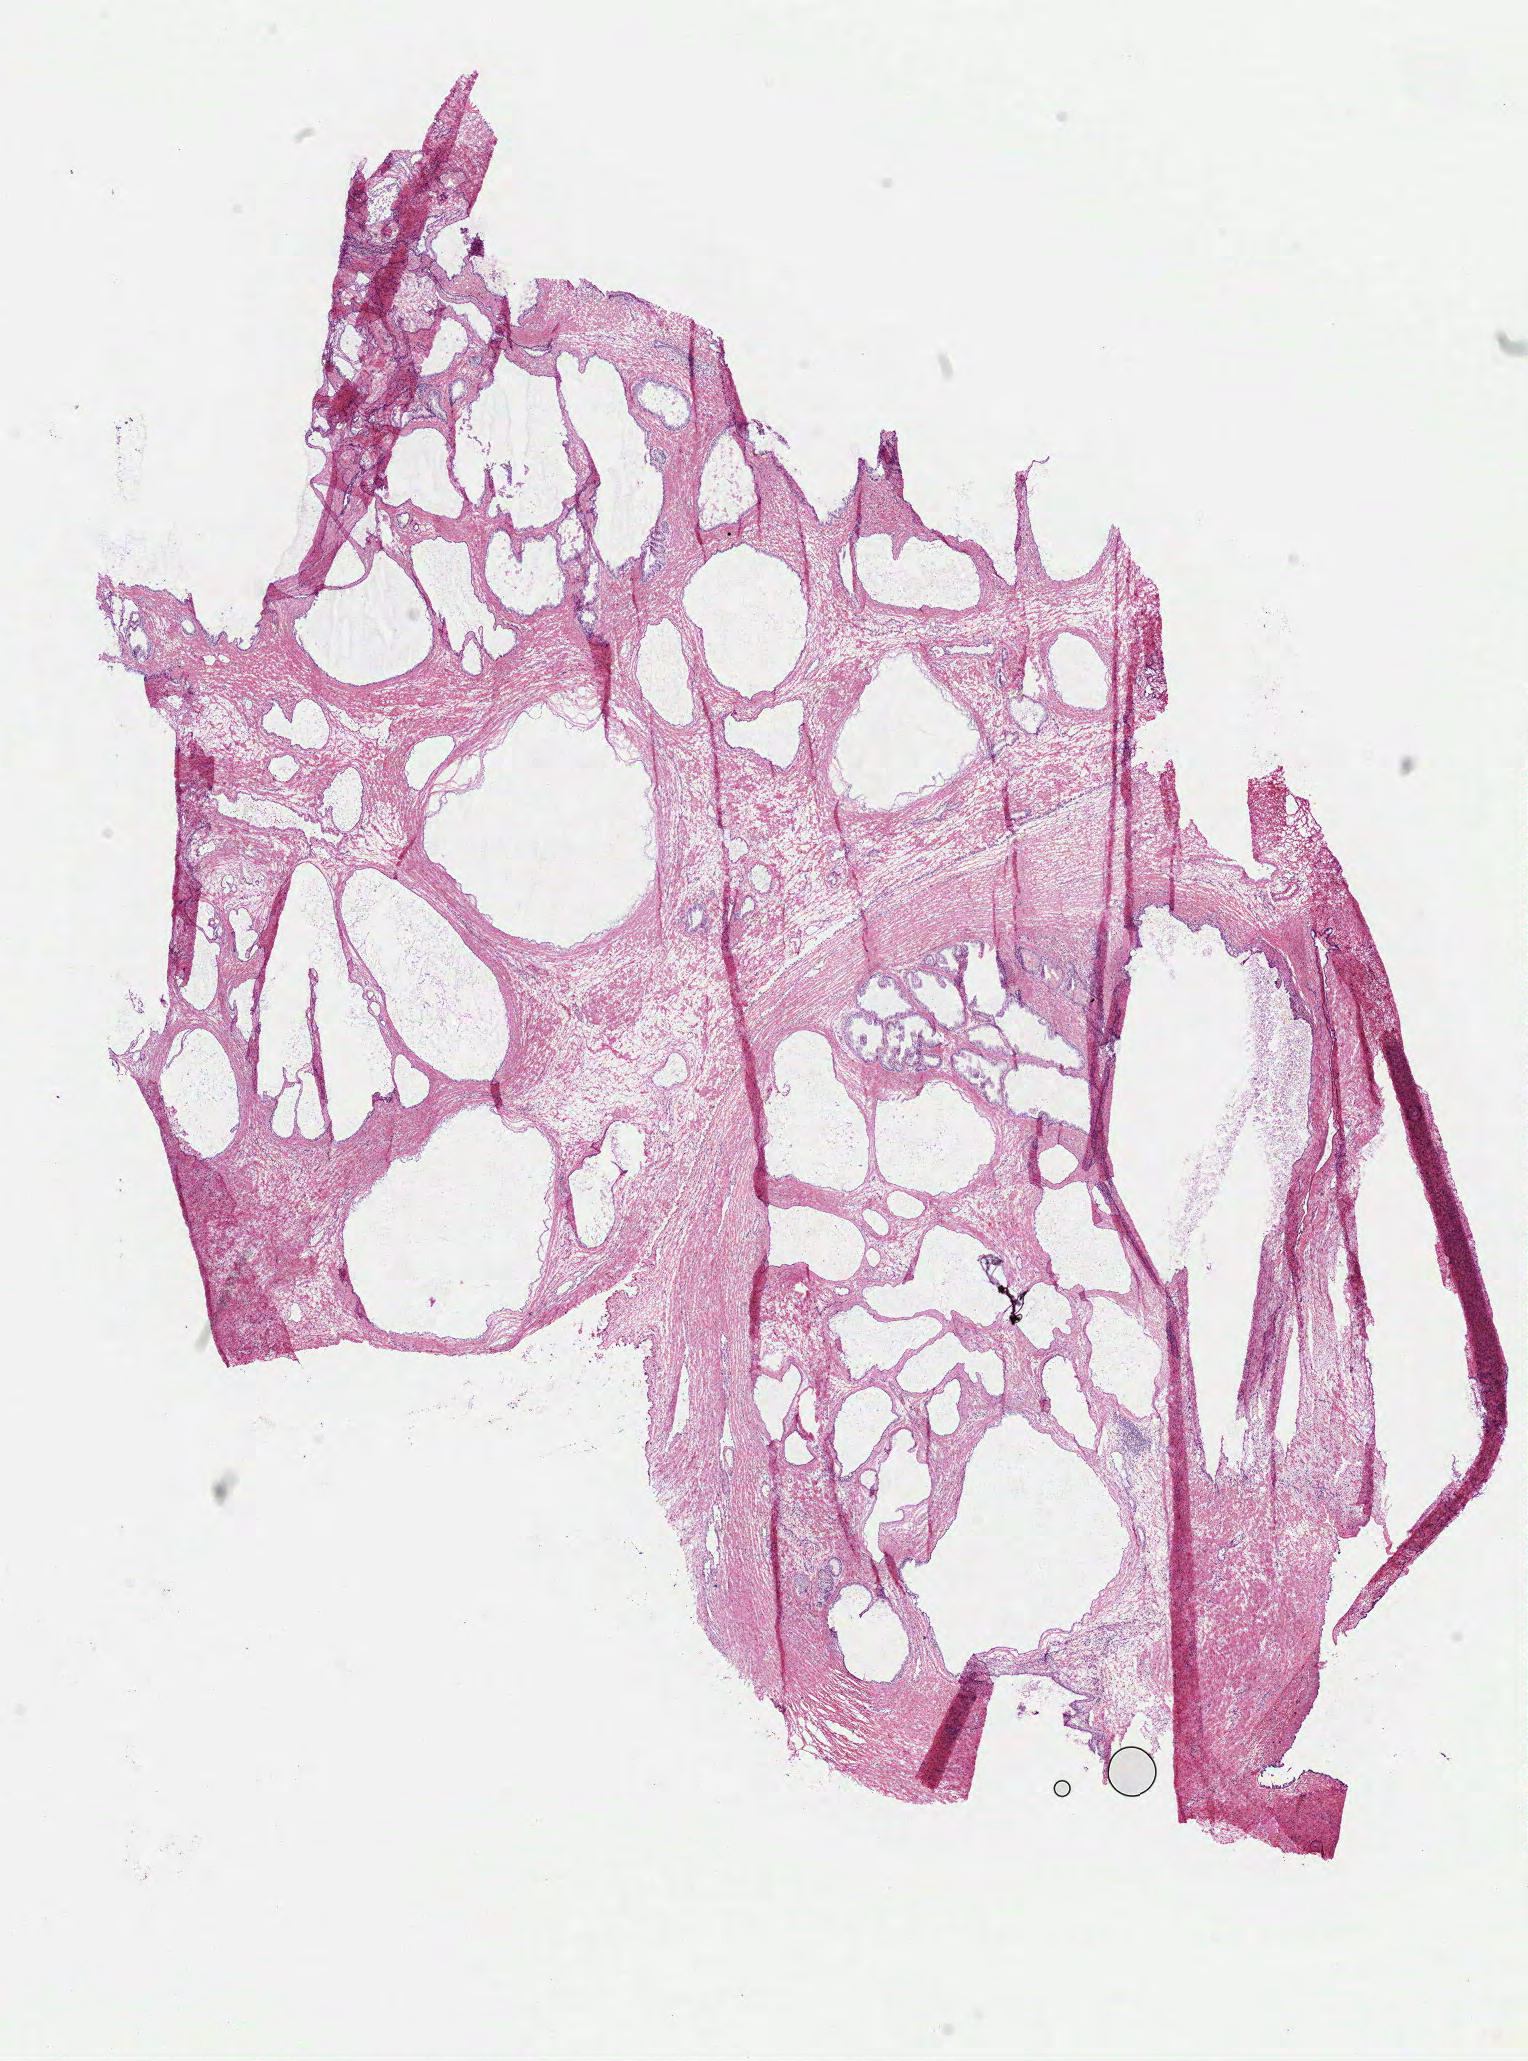
Whole-slide histology image, Hematoxylin and eosin (H&E) stained, shown as a low-resolution overview of the whole scanned area (about 12.3 x 16.6 mm, slide scanned at 40x), frozen section from the top of the tissue portion, solid tissue normal (non-tumour tissue) sample from the prostate. Male, age 62 years at initial diagnosis.
This section: solid tissue normal (non-tumour) sample from the same patient. Patient diagnosis: Acinar cell carcinoma (prostate gland).